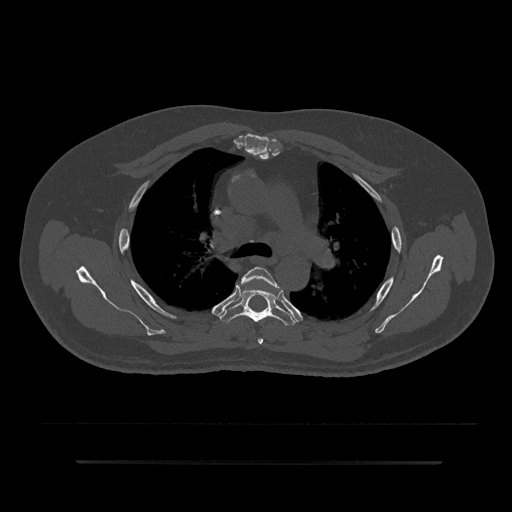
CT including the spine, one axial slice. Slice 587 of 797 in the series (ordered by position). Bone window (W 1800 / L 400 HU). 0.5 mm slice thickness. 512 × 512 image matrix. Patient: male, 59 years. From the clinical record (not read from this slice): primary cancer: bile ducts.
Outlined on this slice (semi-automatically segmented with operator editing):
- T4 vertebra: bounding box (x1, y1, x2, y2) in pixels: (241, 267, 278, 345)
- T5 vertebra: (219, 288, 297, 326)